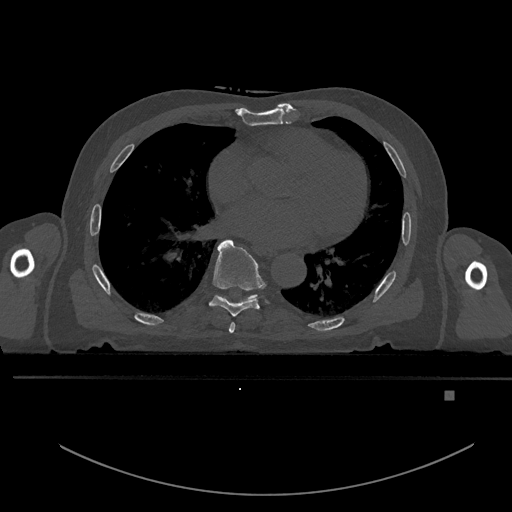
CT including the spine, one axial slice; slice 249 of 969 in the series (ordered by position); bone window (W 1800 / L 400 HU); 0.5 mm slice thickness; 512 × 512 image matrix, field of view 456 × 456 mm. Male patient, age 82 years. From the clinical record (not read from this slice): primary cancer: prostate.
Outlined on this slice (semi-automatically segmented with operator editing):
- T6 vertebra: bounding box <229,322,235,334> (left, top, right, bottom; pixels)
- T7 vertebra: <208,239,269,317>
- T8 vertebra: <216,295,258,303>